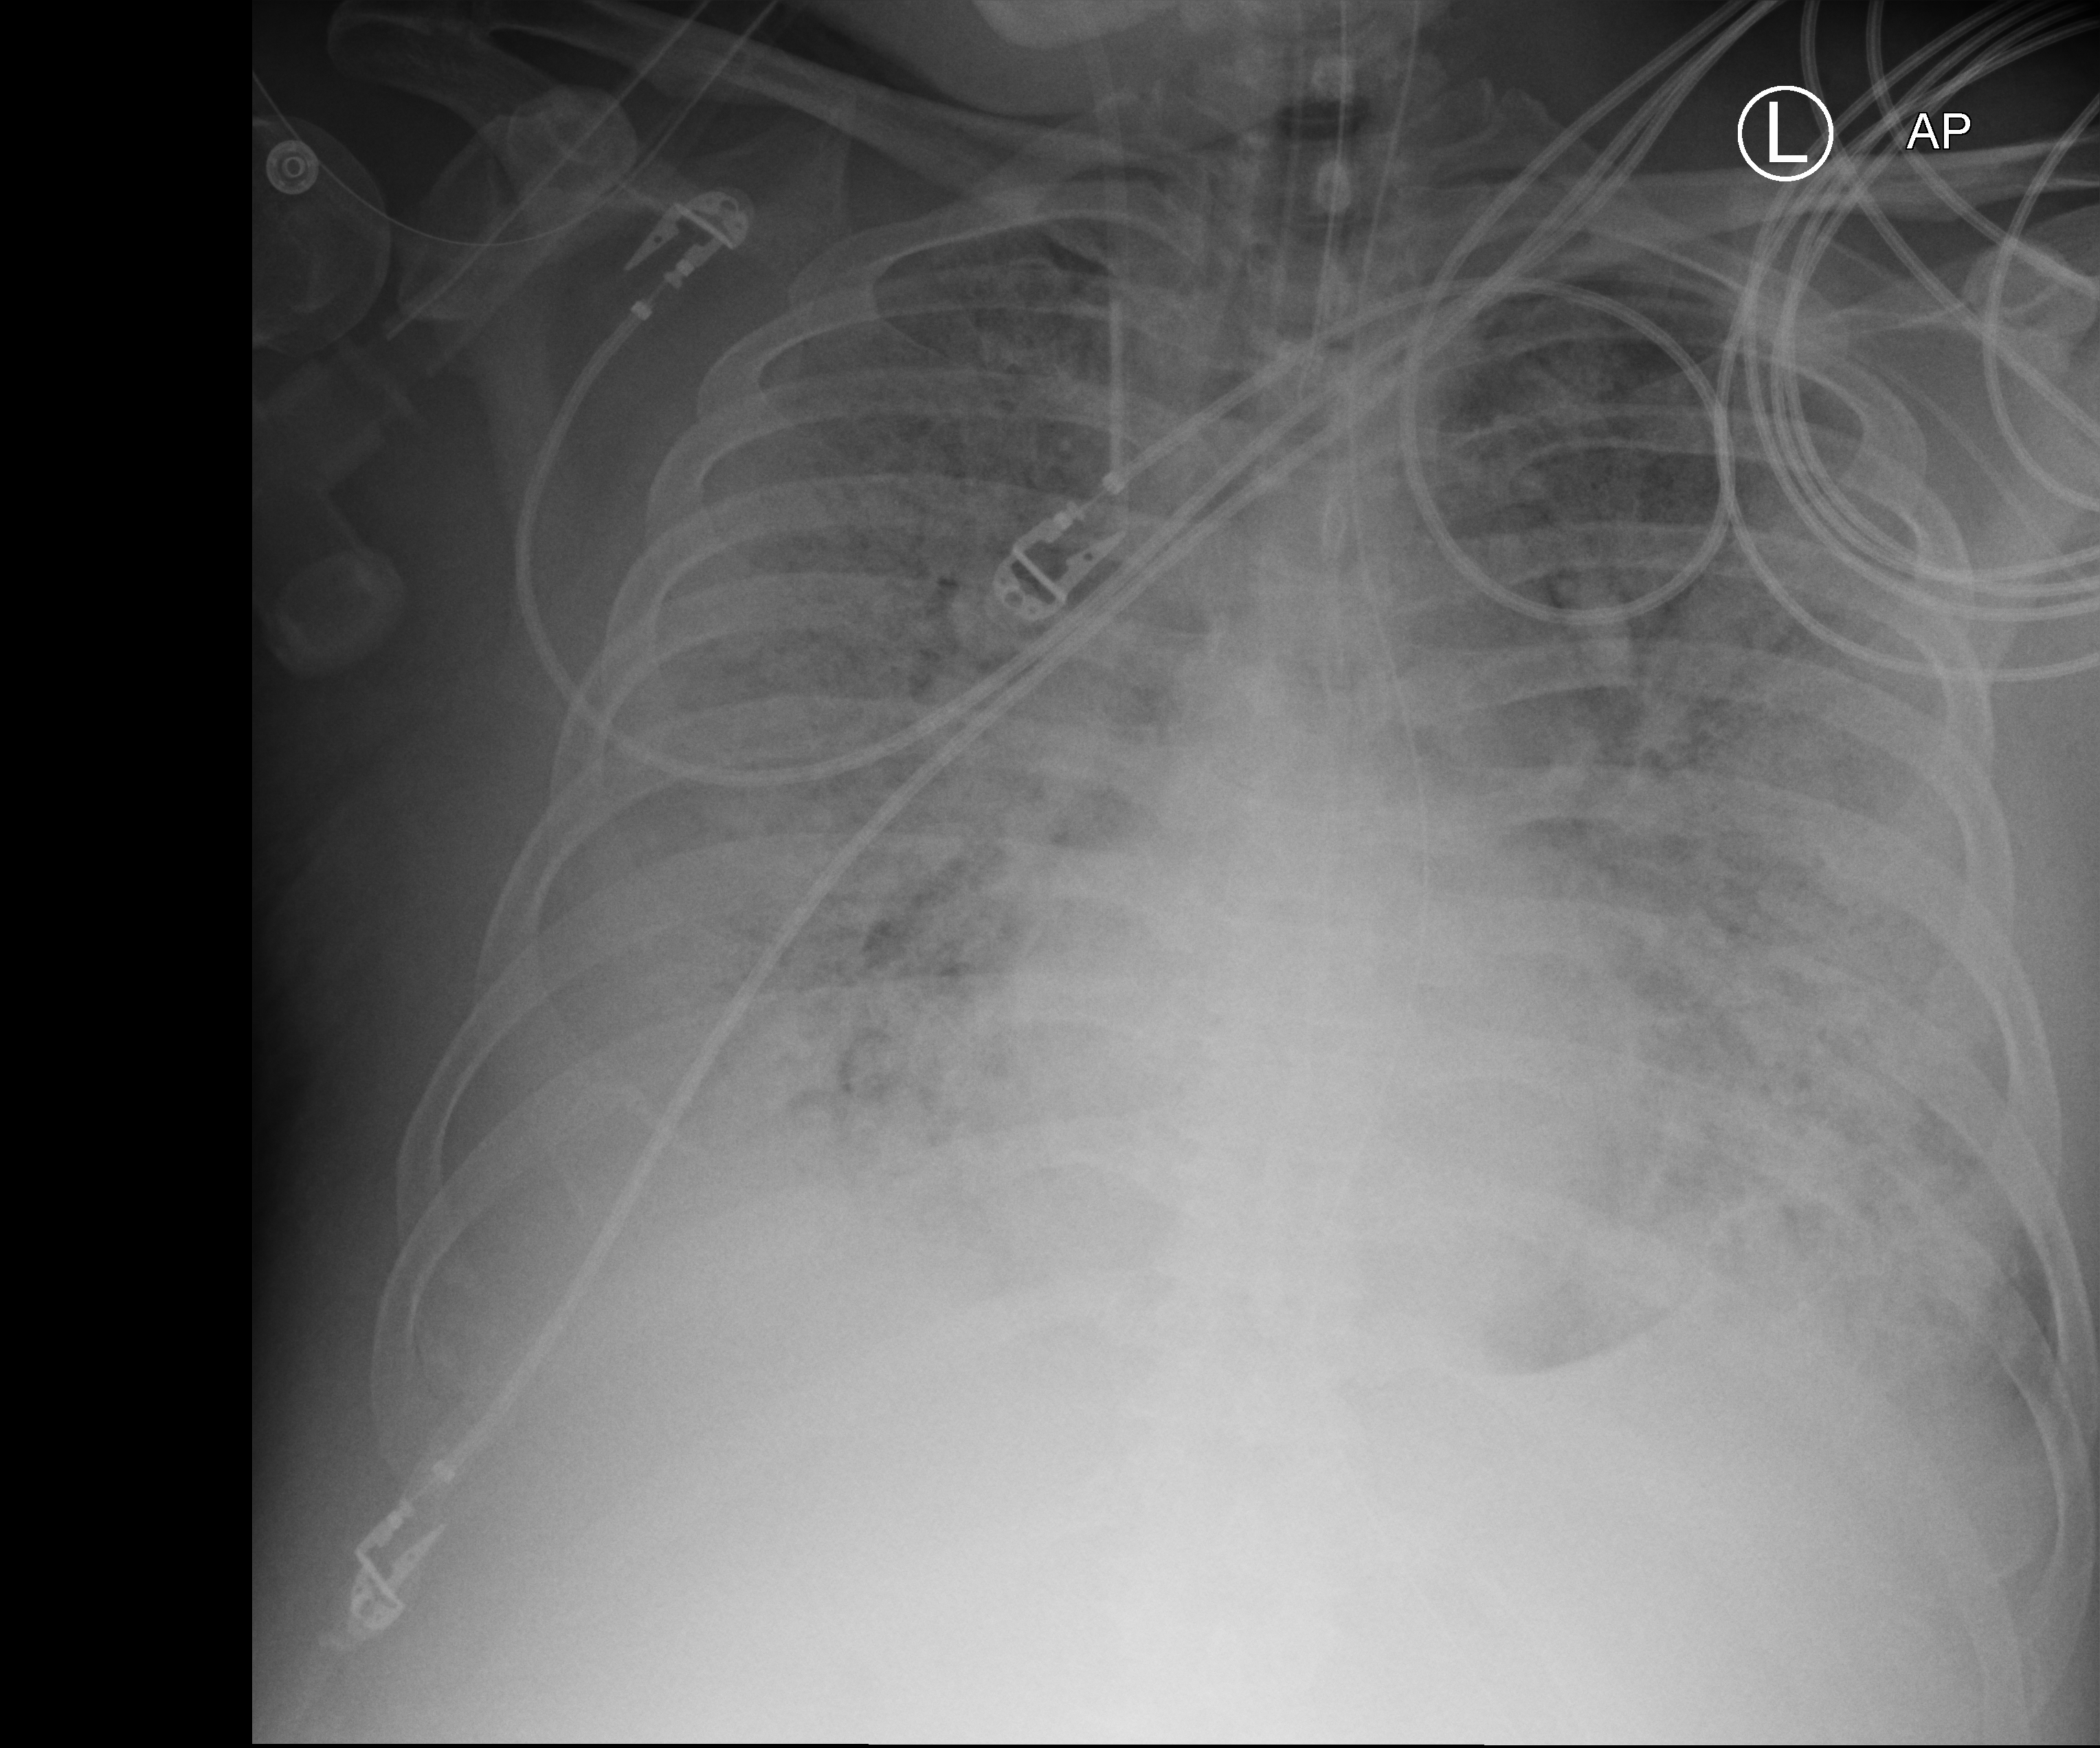
Portable chest radiograph. Male patient hospitalised with COVID-19, age 60–74 years.
Hospital-stay facts (about this admission, not read from this image; timing relative to this image not recorded): COPD (admission record): no; mechanically ventilated during this hospital stay: yes.